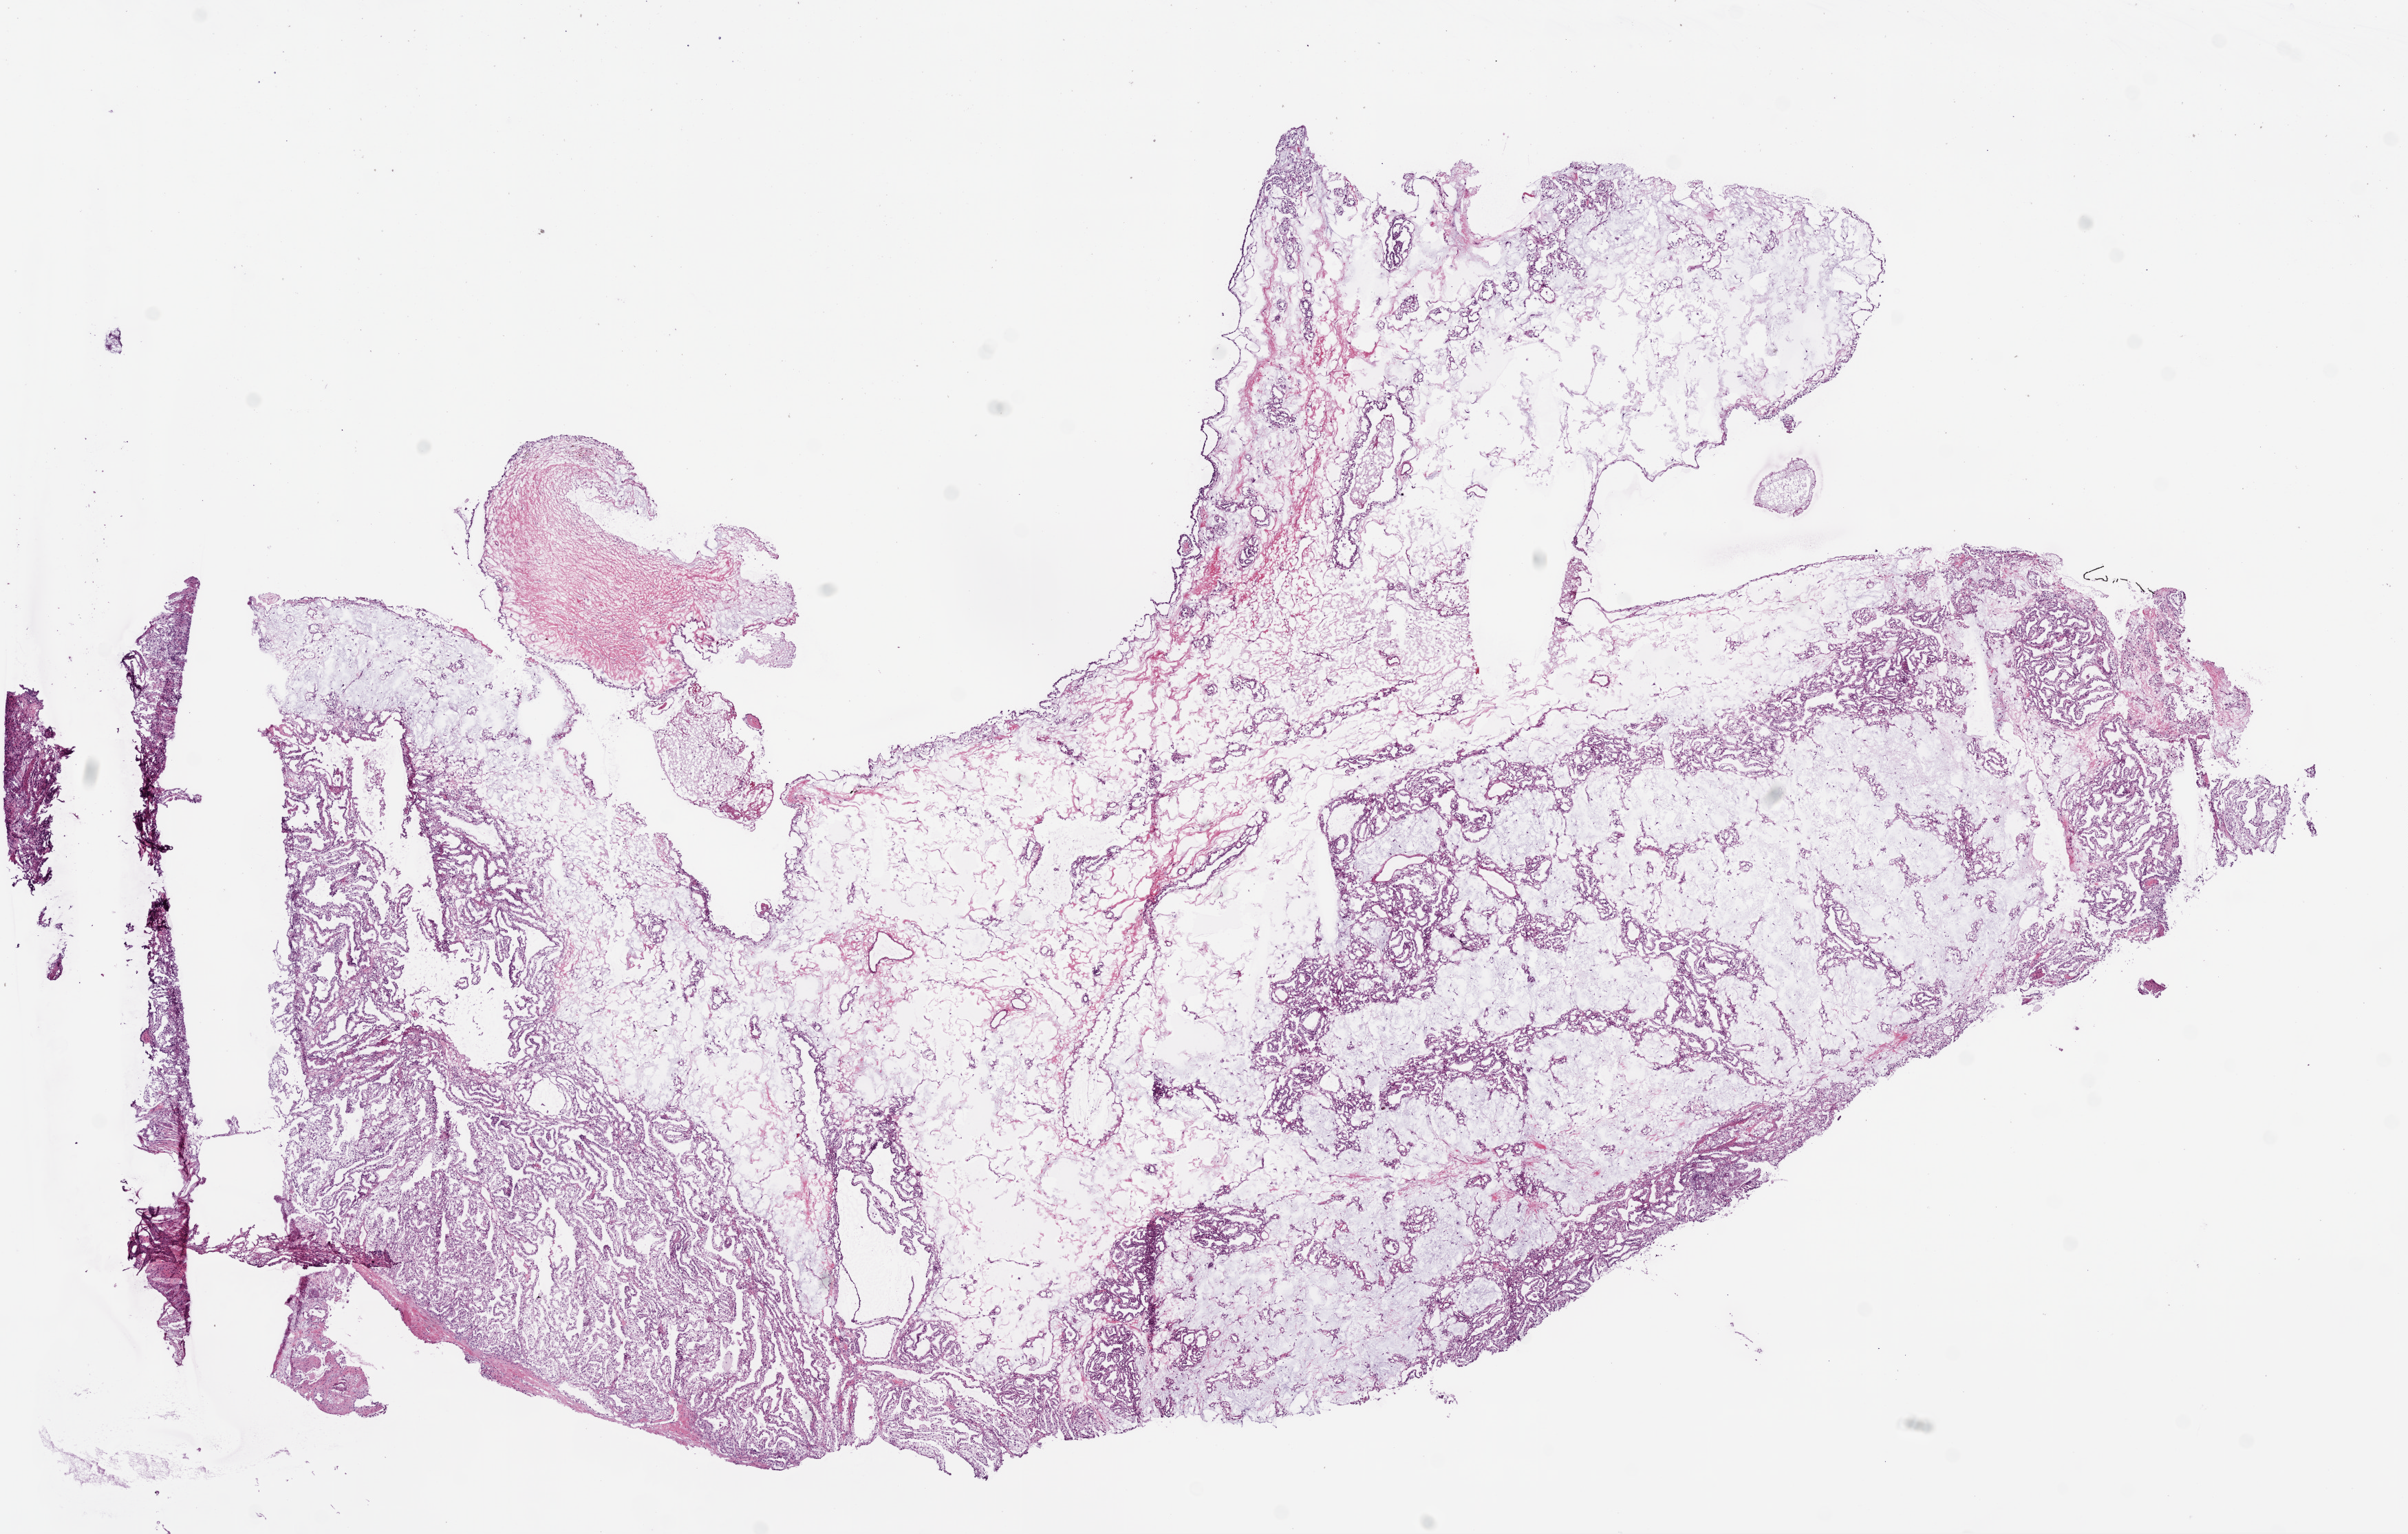
H&E whole-slide image, shown as a low-resolution overview of the whole scanned area (about 14.0 x 8.9 mm, from a 20x scan); frozen section; kidney, primary tumour sample. Male patient; age at initial diagnosis 69 years. Histologic grade: G2 (moderately differentiated). Composition of this section per pathologist review: tumour cells 98%, tumour nuclei 90%, stromal cells 2%, necrosis 0%. Infiltration values recorded for this section: lymphocyte infiltration 1%.
• laterality: left
• histologic diagnosis: Clear cell adenocarcinoma, NOS
• AJCC pathologic stage: I